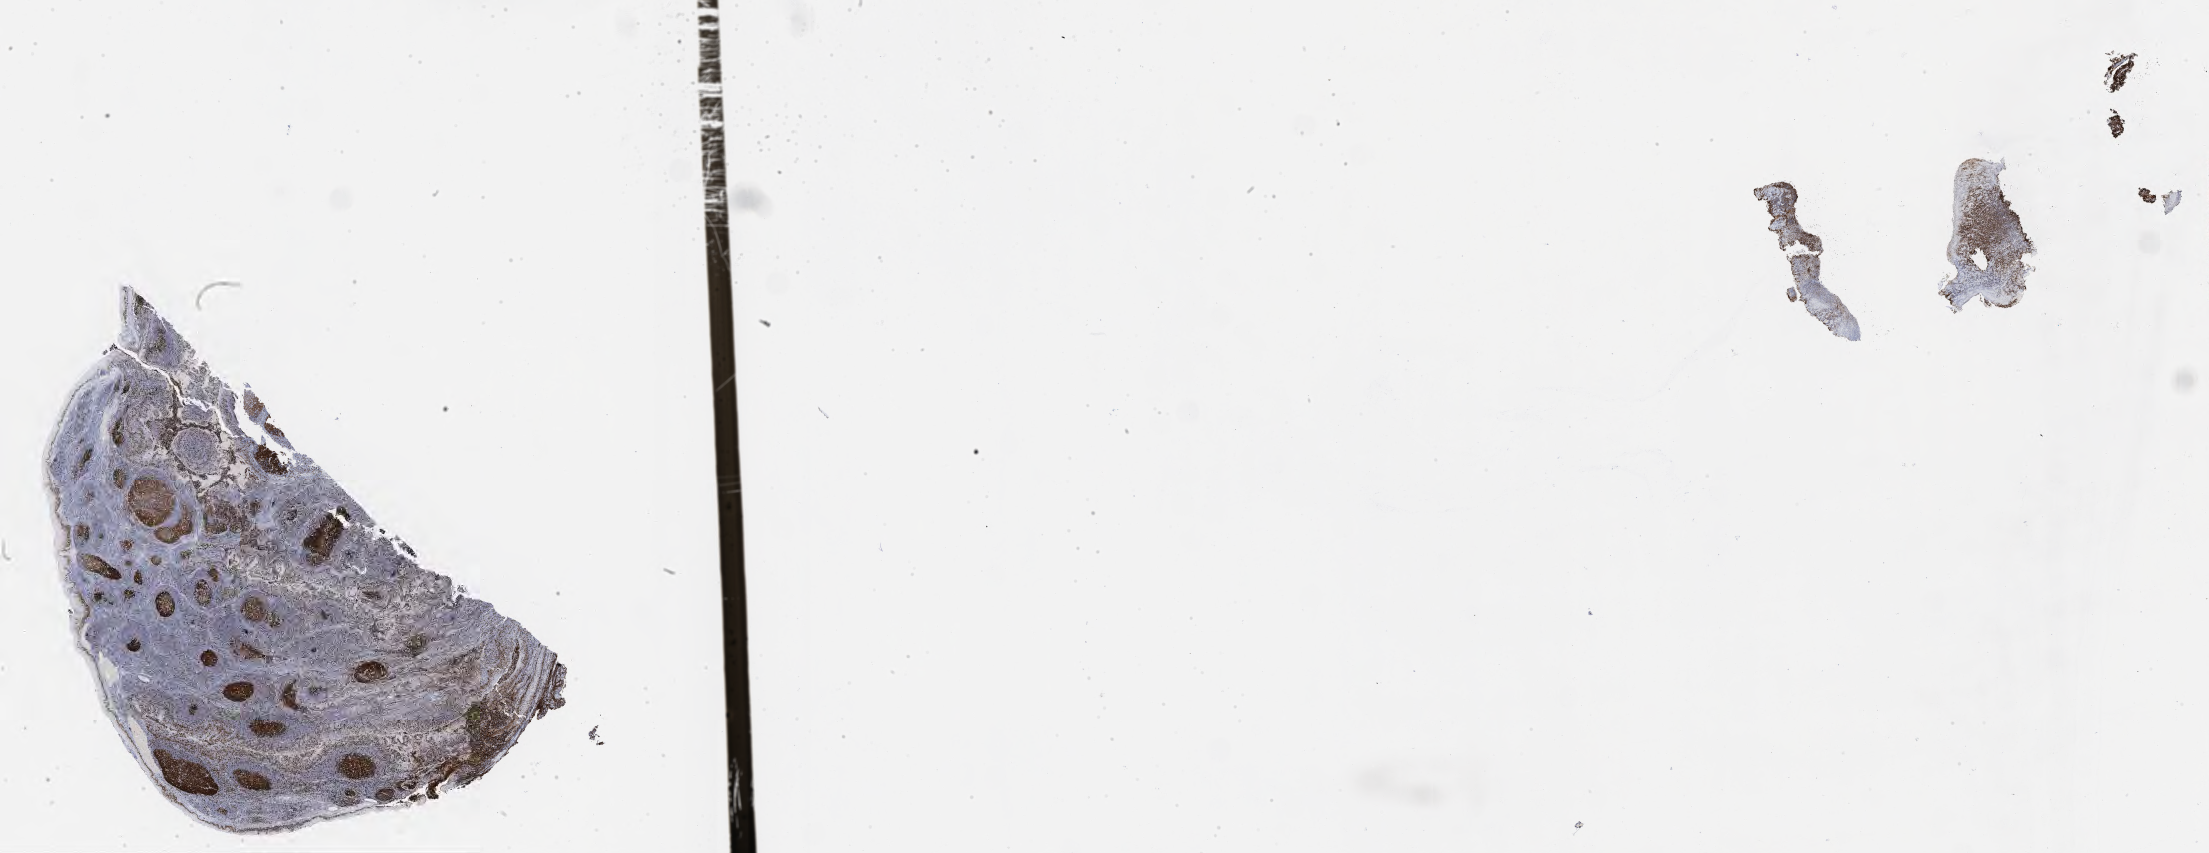
IHC for Ki-67, whole-slide image, whole scanned area (about 35.7 x 13.8 mm) shown as a low-resolution overview; specimen: tumor tissue; site: colon. Patient: male, 28 years old.
Histologic diagnosis: Burkitt lymphoma, NOS.